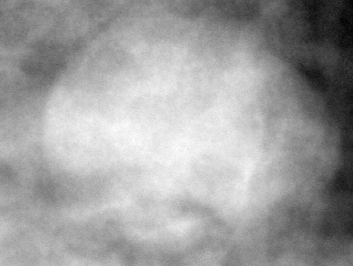
Cropped region of a digitized screen-film mammogram centred on a radiologist-marked abnormality; left breast; CC view.
- Marked abnormality: mass, shape lobulated, margins circumscribed / ill defined; BI-RADS assessment category 4; pathology result (as recorded, not read from the image): benign.